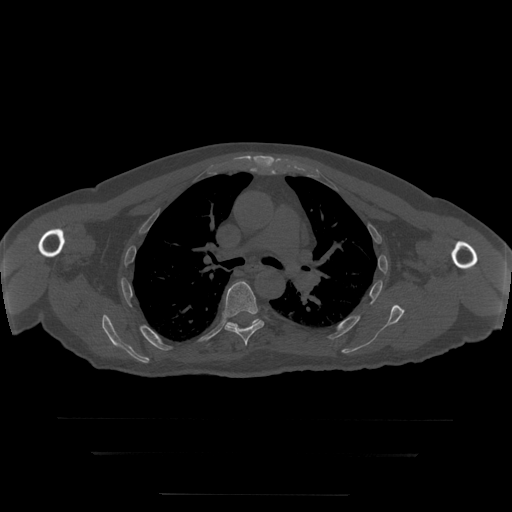
CT including the spine, one axial slice; position 204 of 397 along the scan axis; 120 kVp; bone window (W 1800 / L 400 HU); 1.25 mm slice thickness; 512 × 512 image matrix, field of view 510 × 510 mm. Patient age 73 years. Case-level facts recorded for this patient, not image findings: primary cancer: prostate.
Structures marked on this image (semi-automatically segmented with operator editing):
- T6 vertebra: bounding box [x1, y1, x2, y2] px = [224, 282, 265, 346]
- T7 vertebra: [228, 319, 260, 327]